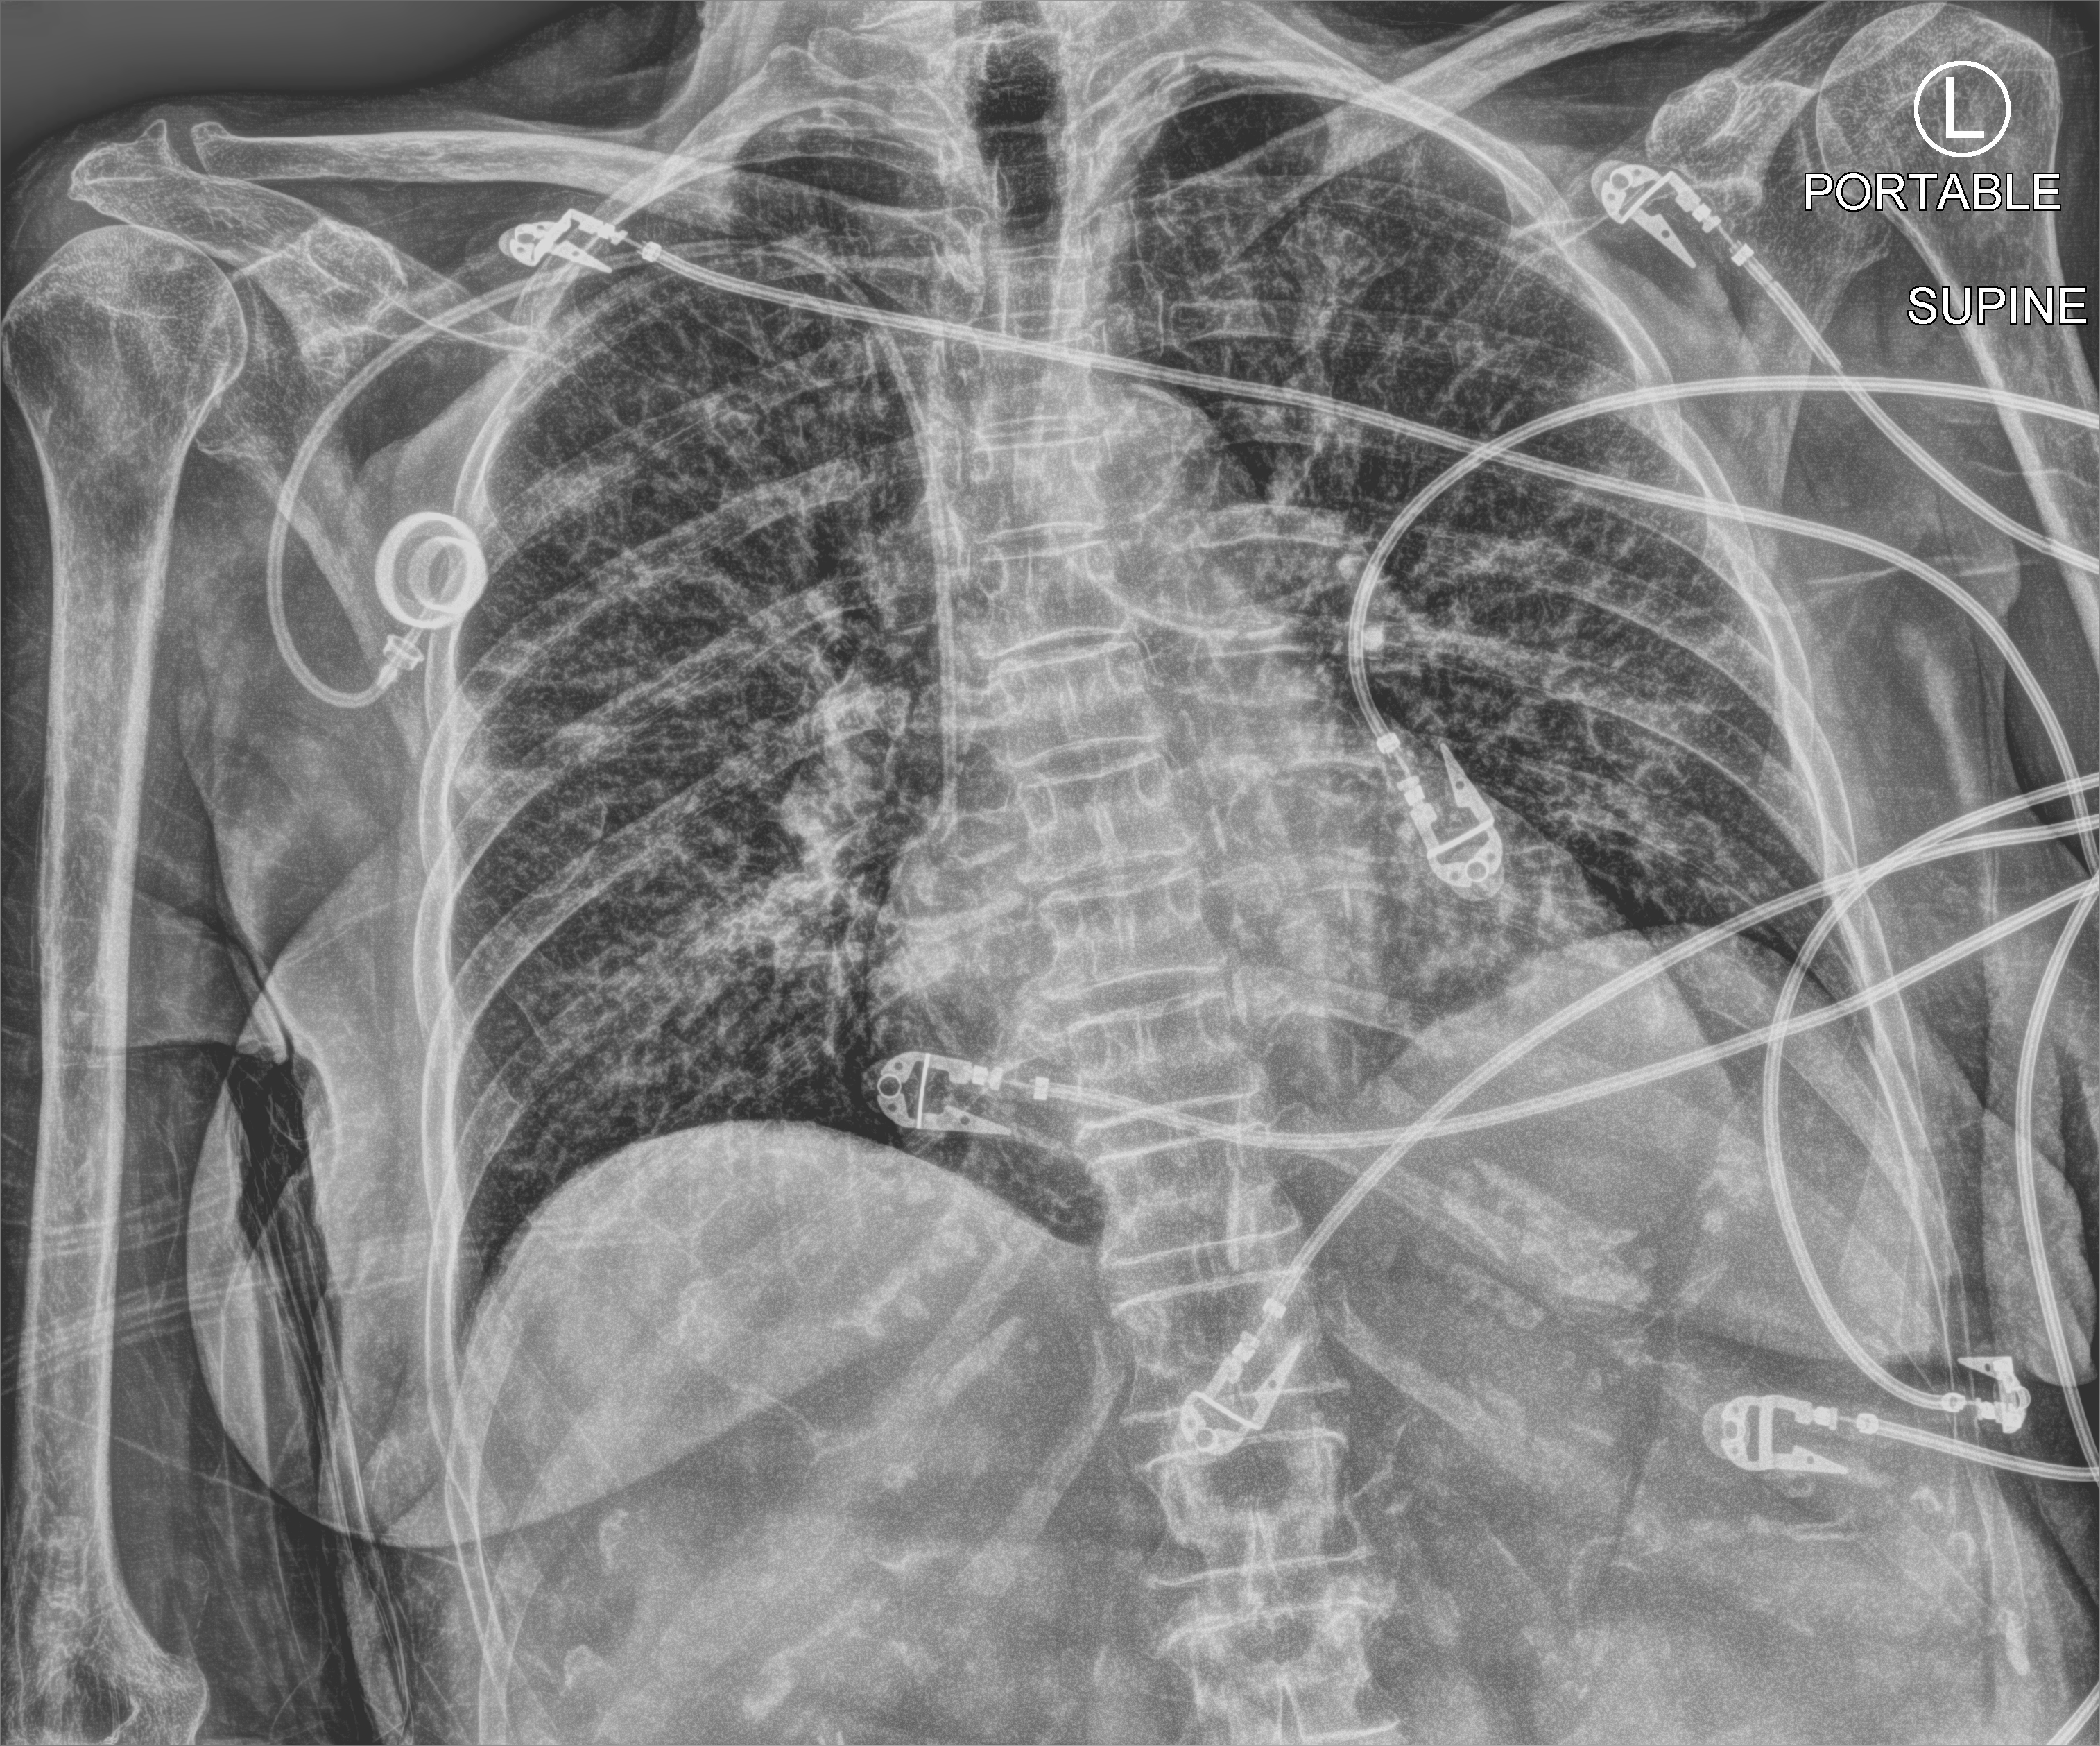
Chest X-ray (portable); anteroposterior (AP) projection. Patient hospitalised with COVID-19; female, aged 75–90 years.
Admission-level facts for this patient (not findings on this image; timing relative to this image not recorded): admitted to intensive care during this hospital stay: yes; mechanically ventilated during this hospital stay: no.